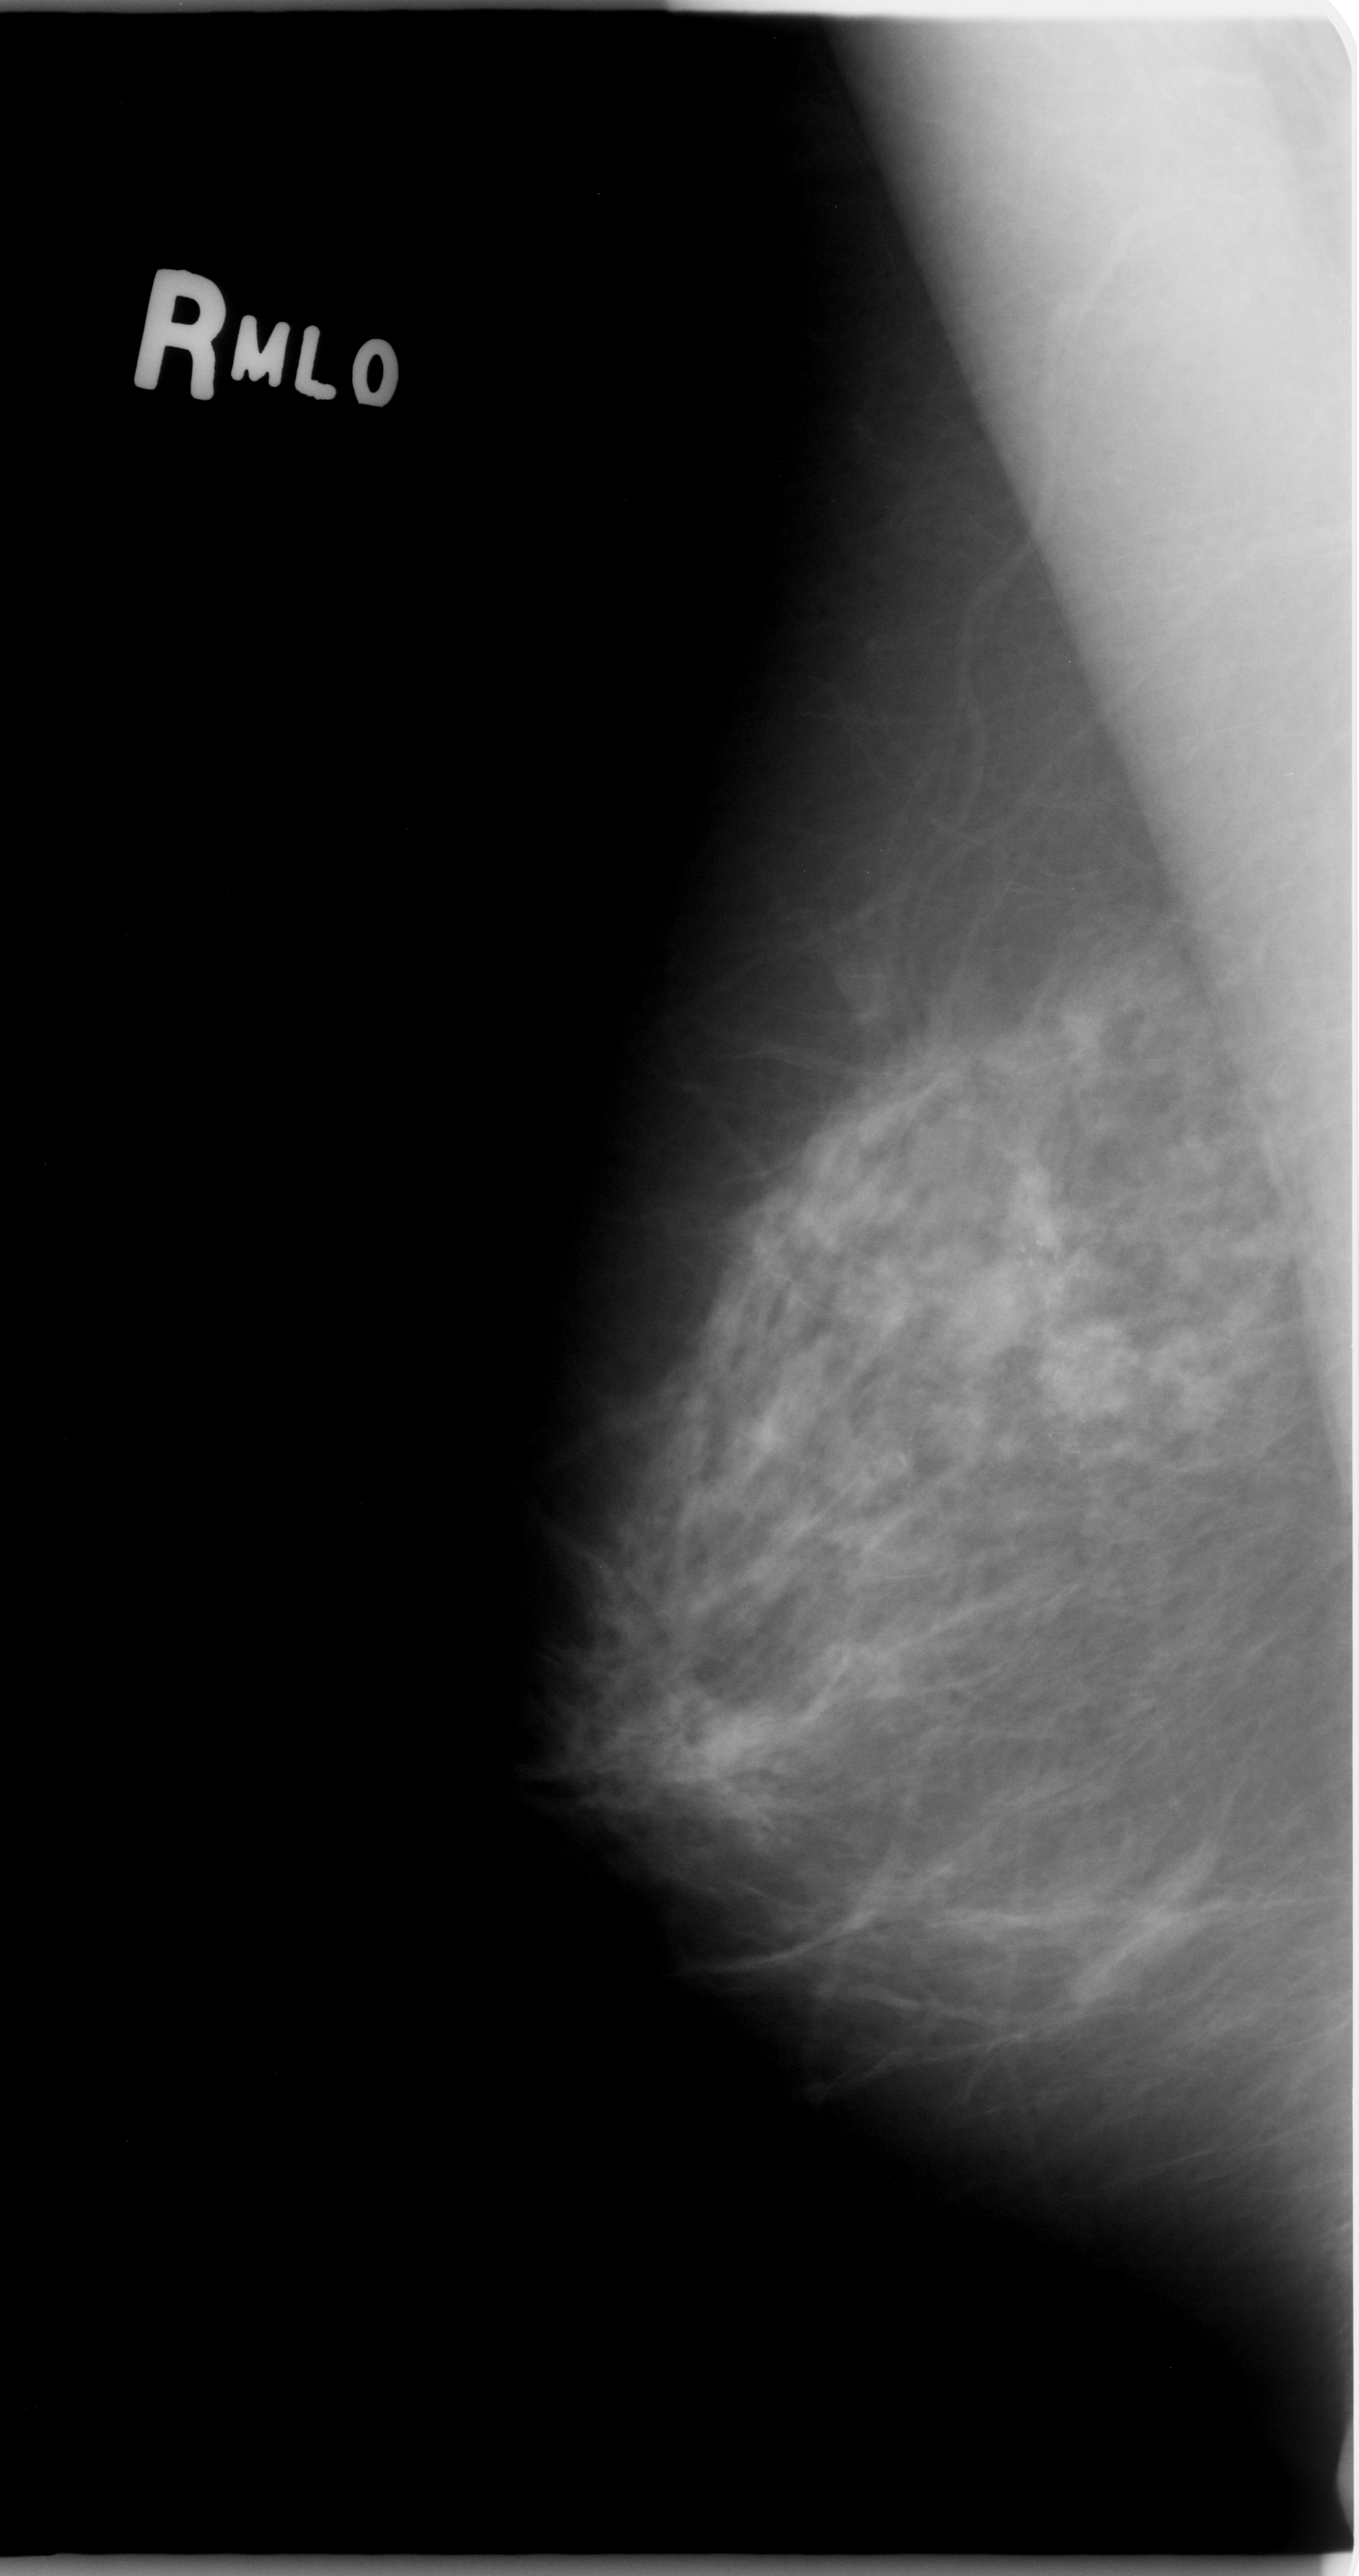
Scanned film-screen mammogram; right breast; mediolateral oblique (MLO) view; 1359 × 2576 image matrix.
Expert-marked regions of interest on this film, with their recorded descriptors:
- calcifications, morphology pleomorphic, distribution clustered; BI-RADS assessment category 5; subtlety rating 5 on a 1 (subtle) to 5 (obvious) scale; pathology result (as recorded, not read from the image): malignant: box from (x=885, y=1137) to (x=1218, y=1559) px